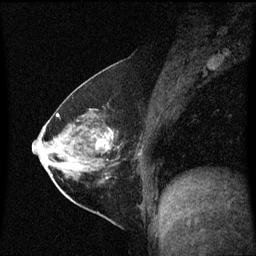
Breast MRI (dynamic contrast-enhanced), one sagittal slice; position 27 of 60 along the scan axis; dynamic contrast-enhanced series, image 2 of 3 at this slice position (ordered by acquisition); 1.5 T; TE 4.2 ms, TR 8.4 ms; 256 × 256 image matrix. Patient: female, 54 years. From the clinical record (not read from this slice): setting: breast cancer imaged before/during neoadjuvant chemotherapy; receptor status: HER2-positive.
Outlined on this slice (semi-automatic segmentation, software-assisted and operator-edited):
- analysis volume of interest (the breast-tissue region the enhancement analysis was run in; not a lesion): bounding box <59,115,141,199> (left, top, right, bottom; pixels)
- tumour enhancement mask (voxels above the 70 % enhancement threshold inside the analysis volume of interest): <92,133,111,151>